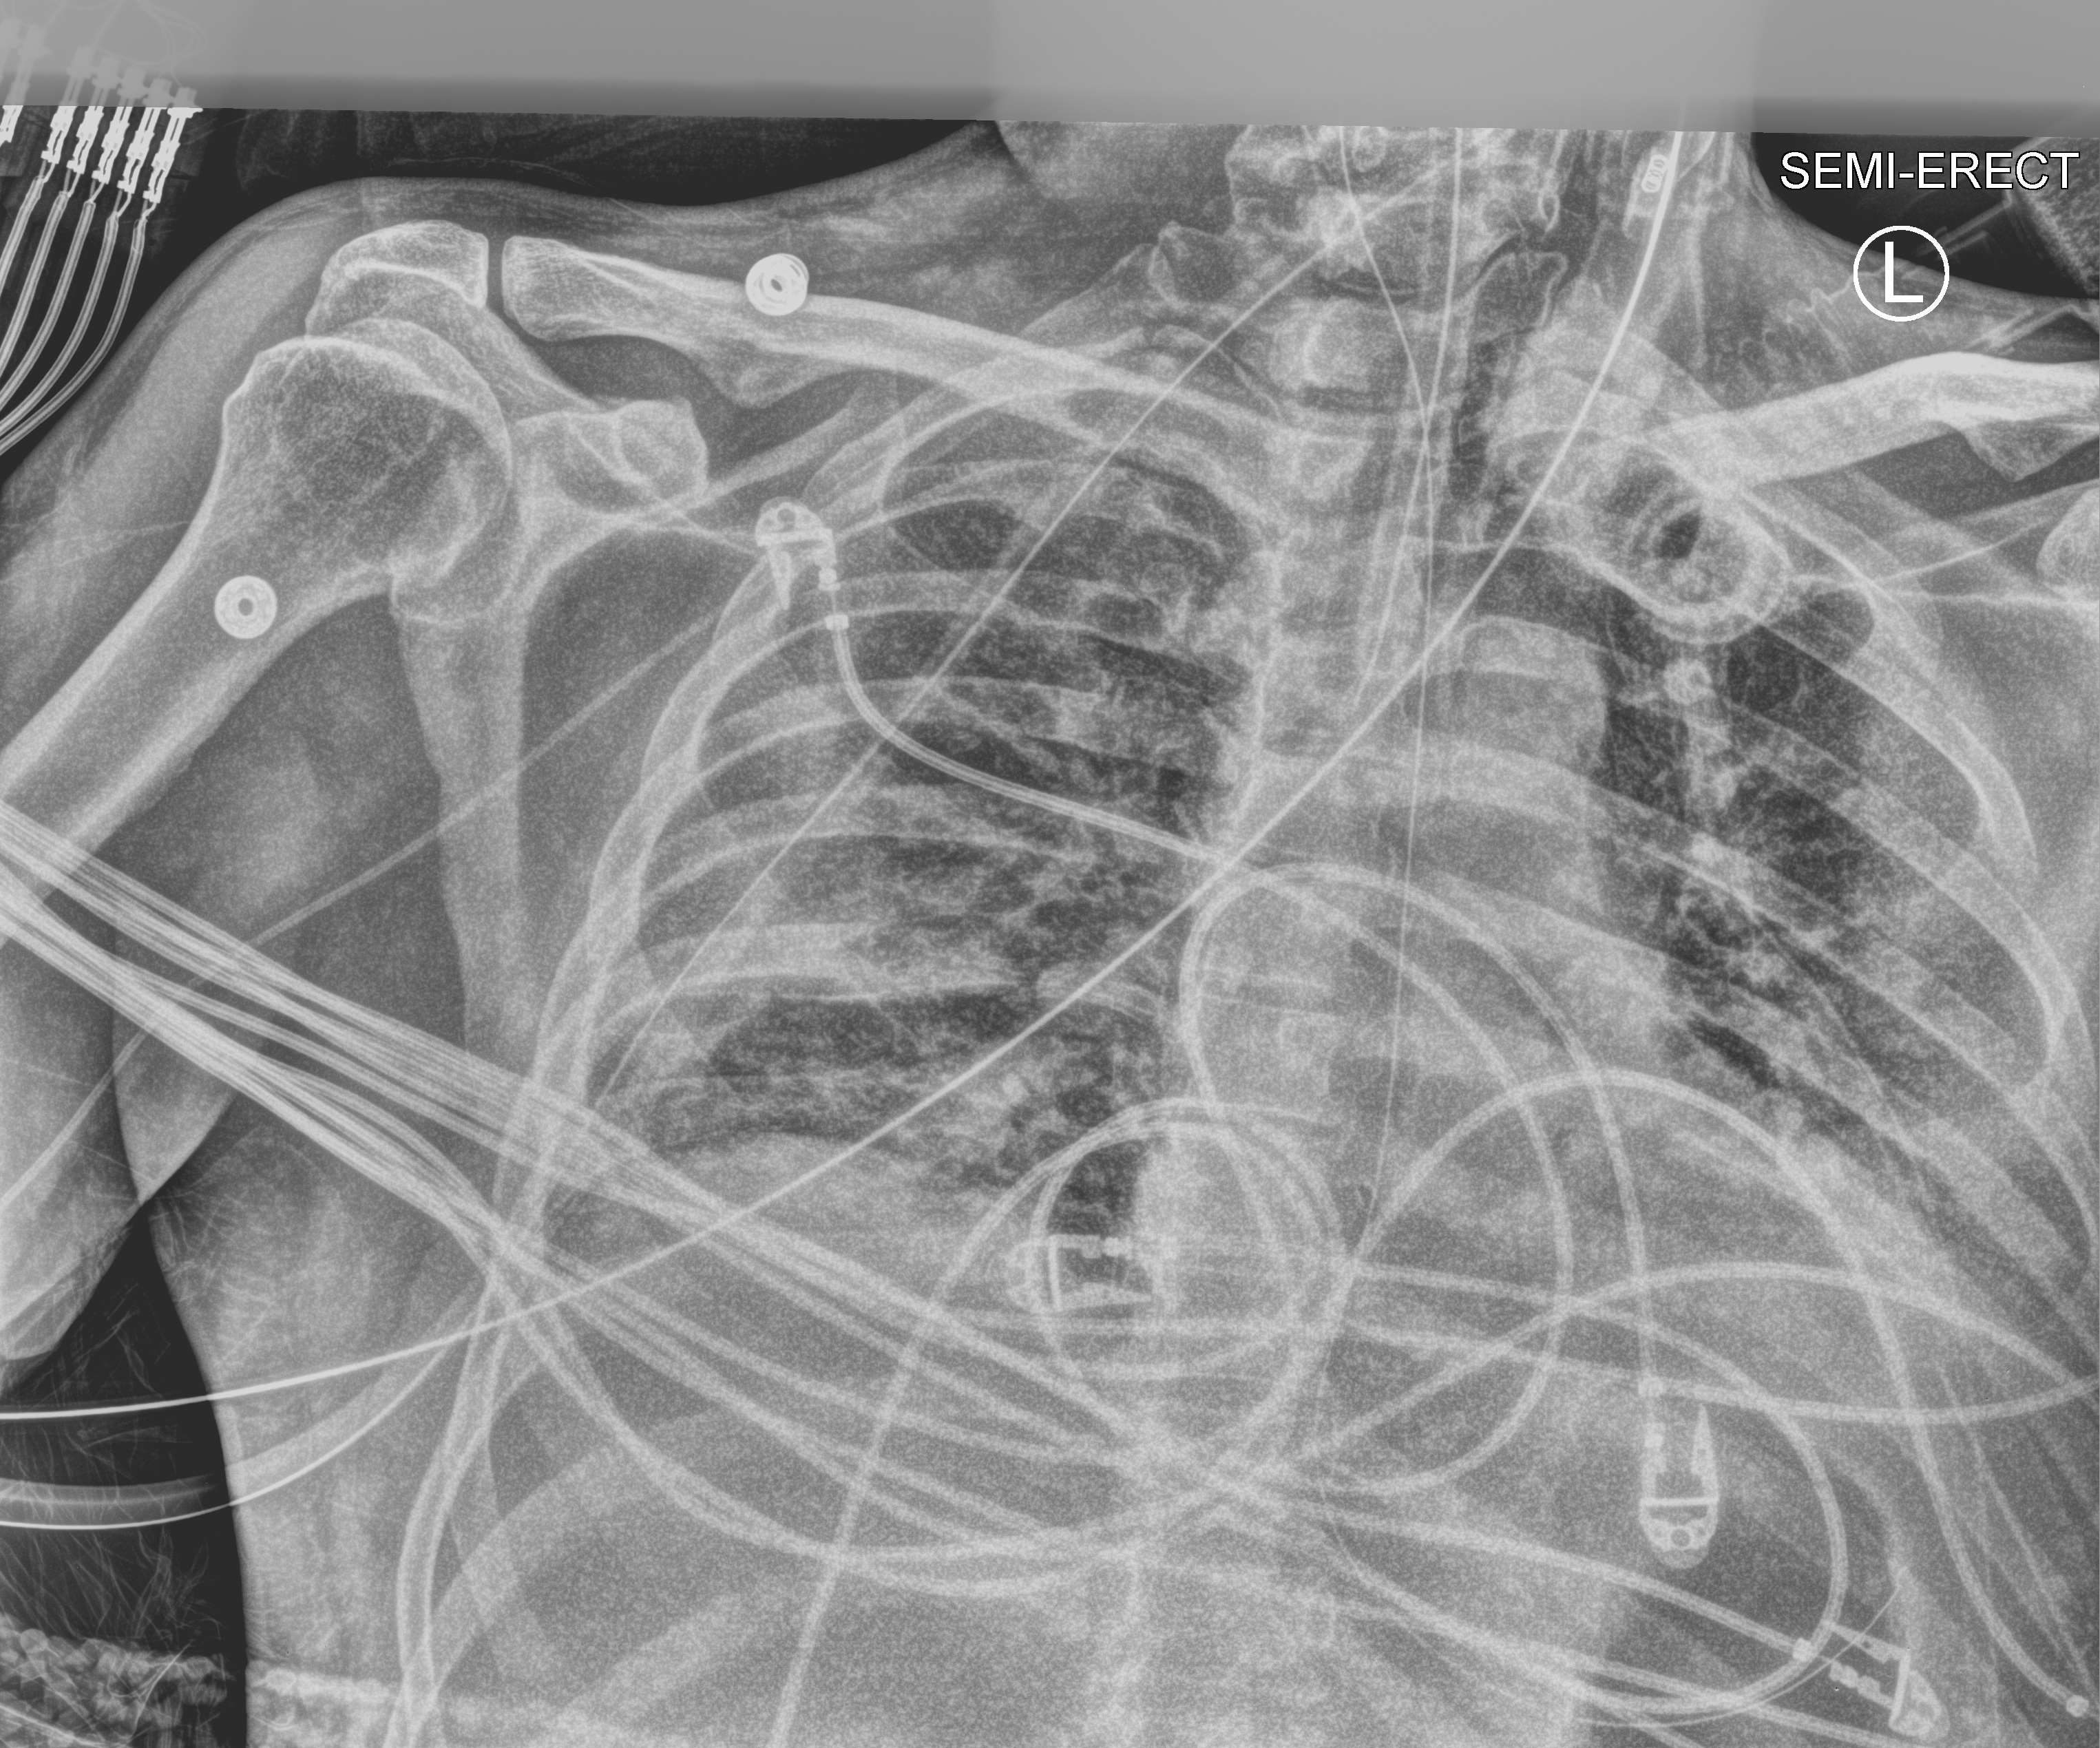
Bedside chest radiograph (computed radiography); anteroposterior (AP) projection. Male patient hospitalised with COVID-19, age 60–74 years.
Hospital-stay facts (about this admission, not read from this image; timing relative to this image not recorded):
- admitted to intensive care during this hospital stay: yes
- smoking status (admission record): never
- mechanically ventilated during this hospital stay: yes